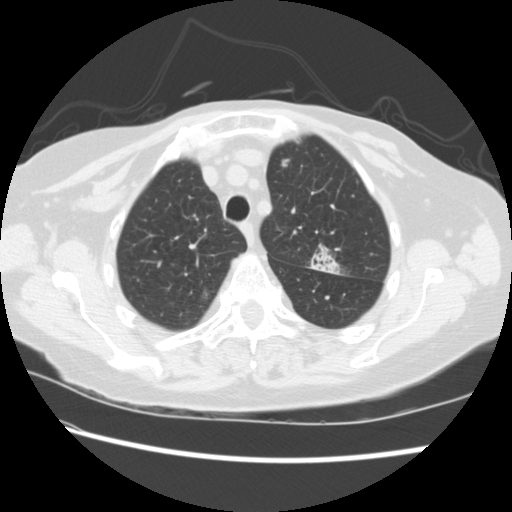
Low-dose screening chest CT, axial slice; baseline screening round; lung window (W 1500 / L -600 HU); 2.5 mm slice thickness; standard (soft-tissue) reconstruction kernel (STANDARD); 512 × 512 image matrix. Female participant, aged 74 years at enrolment. Former smoker at enrolment.
• Expert-annotated lung lesion, bounding box [x1, y1, x2, y2] px = [297, 238, 347, 280].
• The screening reader recorded 2 non-calcified nodules or masses ≥4 mm on this exam (left upper lobe, right lower lobe); which of them this box marks is not recorded.